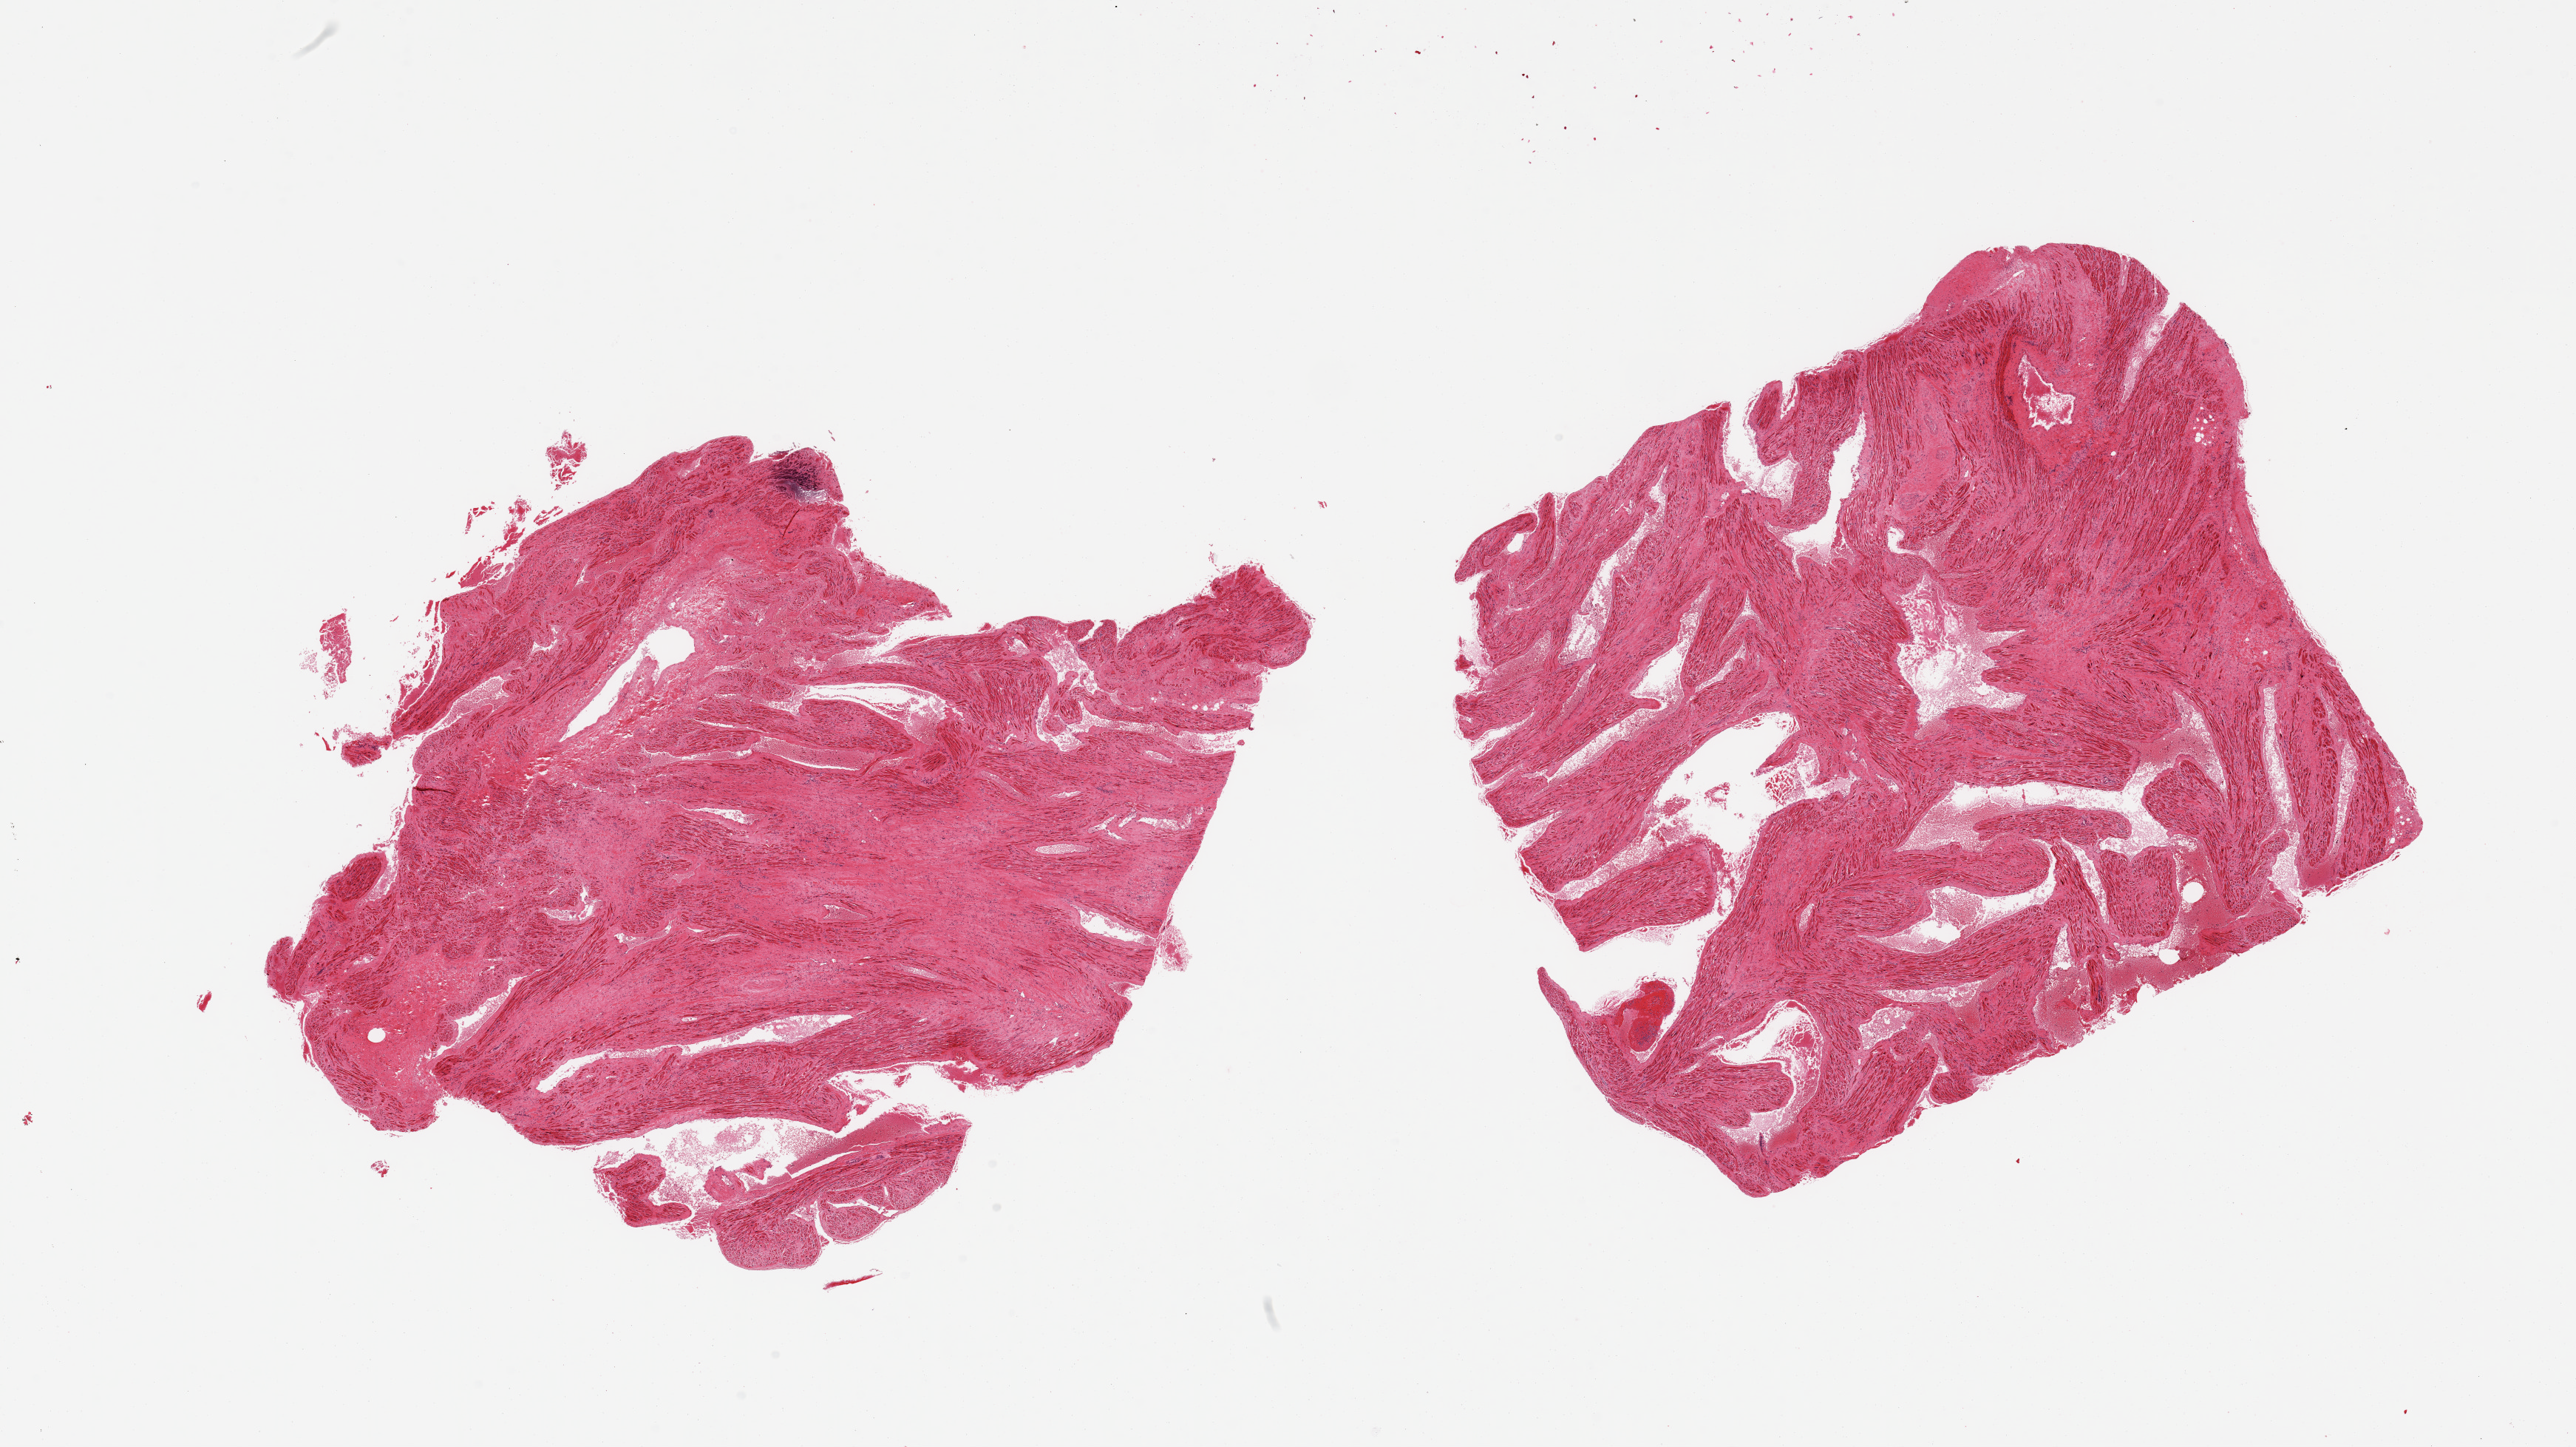
Hematoxylin and eosin (H&E) whole-slide image, brightfield — a low-resolution overview of the entire scanned area, about 27.6 x 15.5 mm, PAXgene-fixed paraffin-embedded (PFPE) section, section of auricular appendage (target tissue), tissue donor sample. Donor sex: male.
• reviewer comment on this tissue sample: 2 pieces; high interstitial fibrous content, 40%